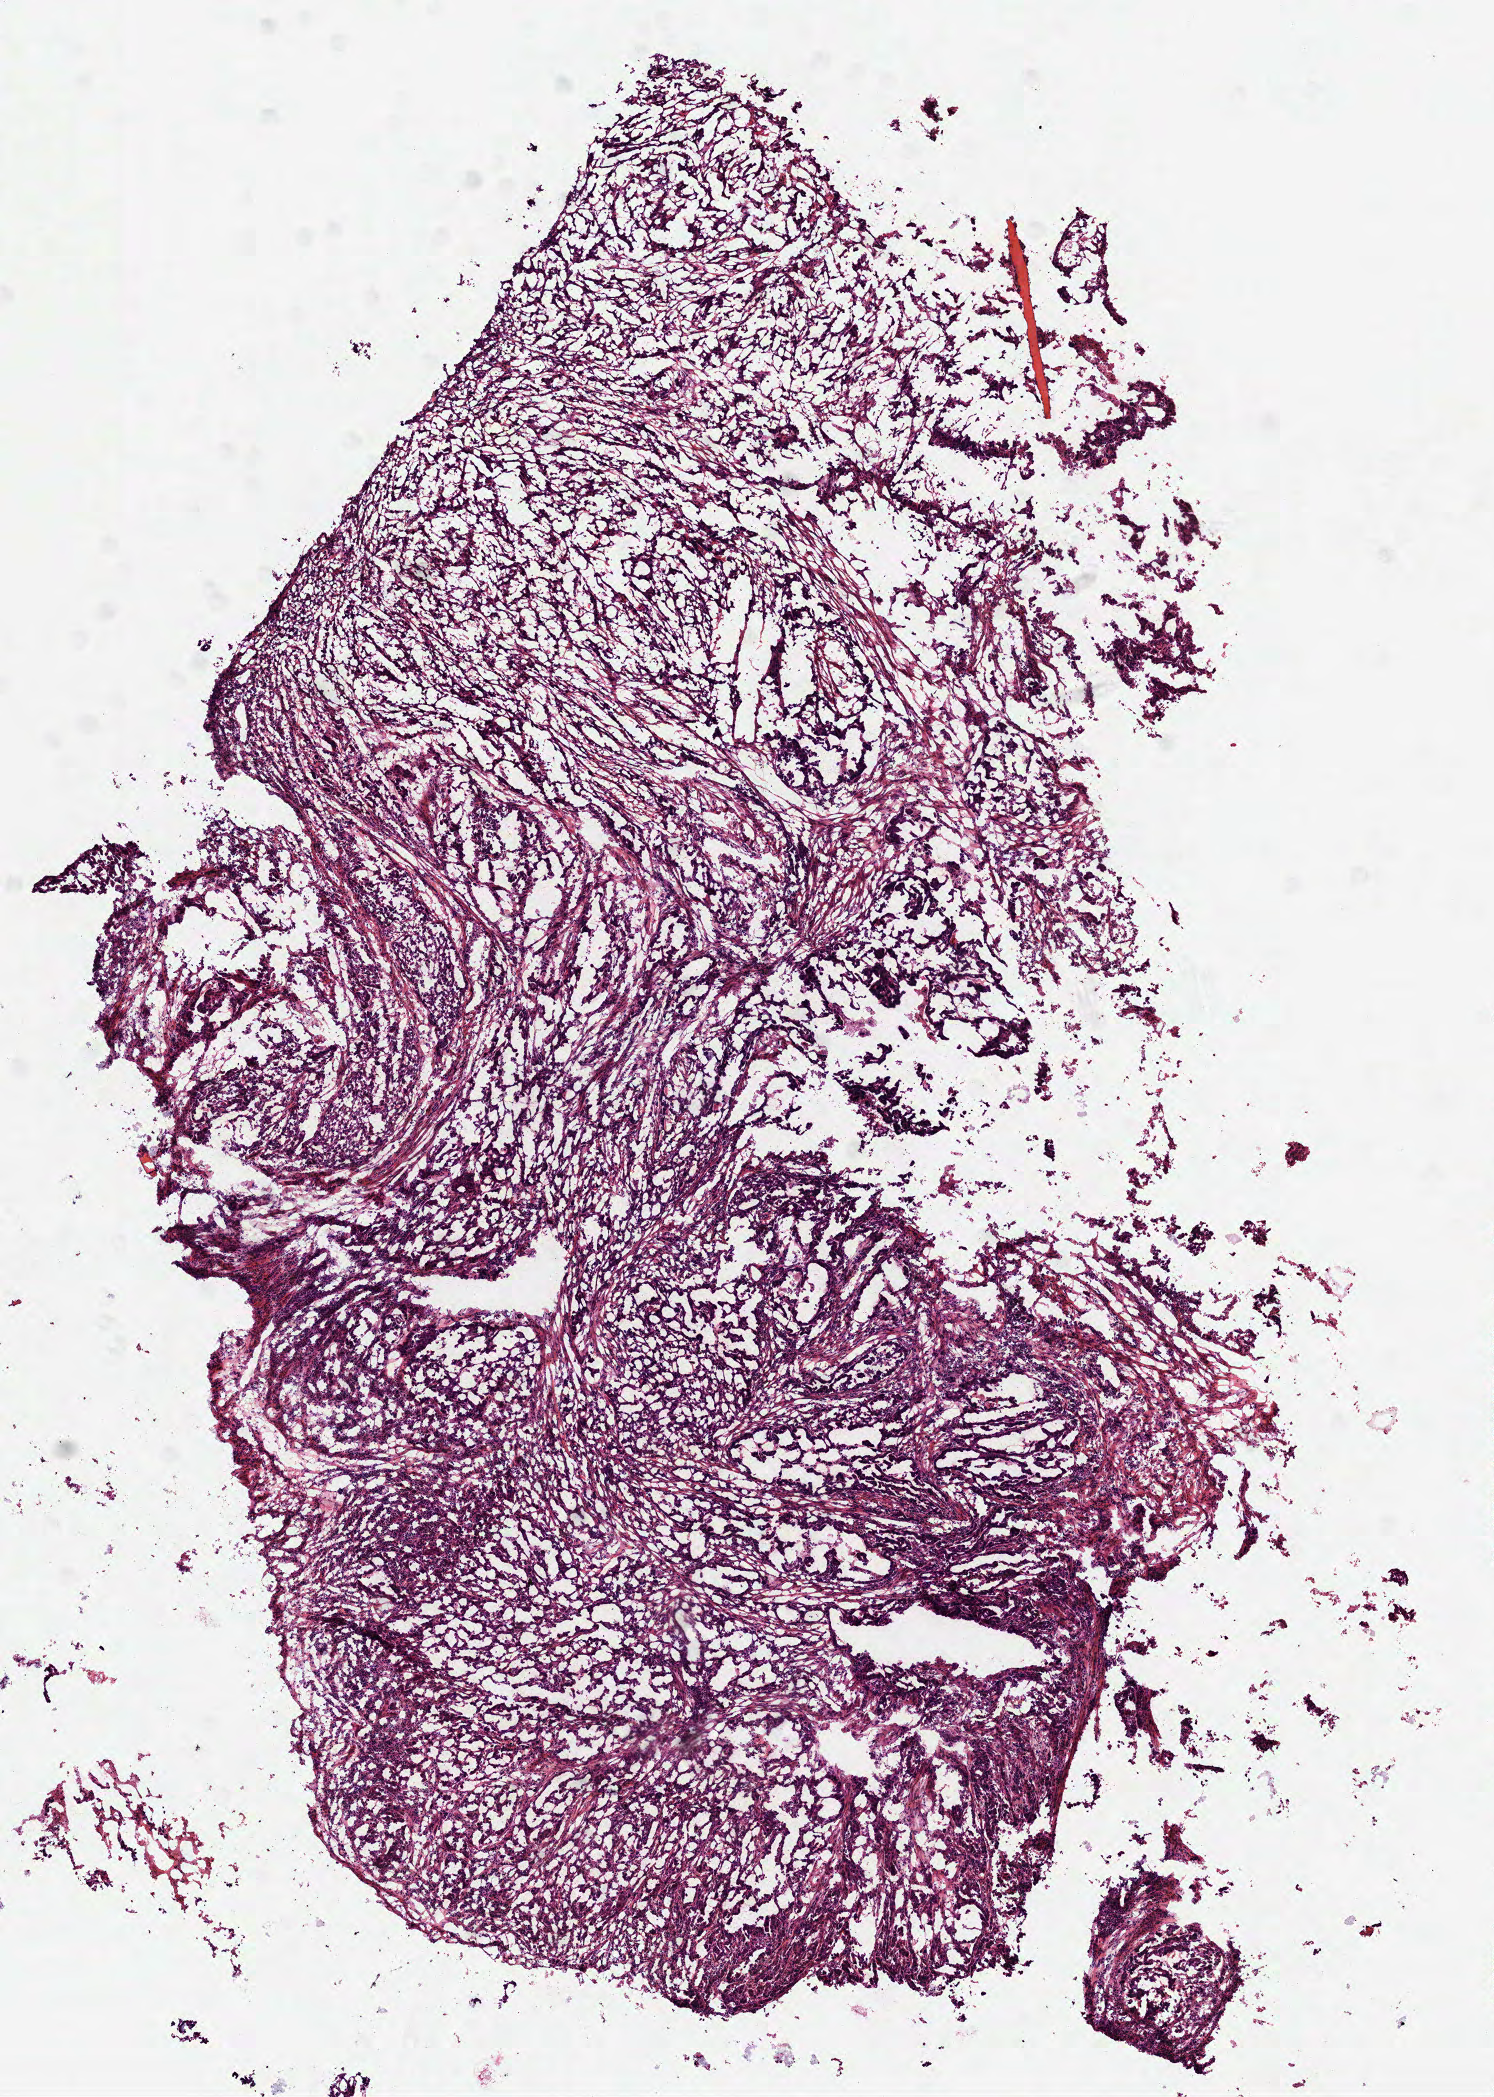
H&E whole-slide image, shown as a low-resolution overview of the whole scanned area (about 6.0 x 8.5 mm, slide scanned at 40x). Frozen section. Primary tumour sample from the stomach. Female patient; age at initial diagnosis 82 years. Histologic grade: G3 (poorly differentiated). Composition of this section per pathologist review: tumour cells 85%, tumour nuclei 75%, normal cells 0%, stromal cells 15%, necrosis 0%.
* histologic diagnosis: Mucinous adenocarcinoma (gastric antrum)
* AJCC pathologic stage: IIIA (6th edition)
* lymph nodes positive (case pathology): 2 of 2 examined